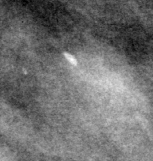
Crop from a digitized film mammogram around one marked abnormality, left breast, CC view, BI-RADS breast density category 3 (scale 1–4).
Calcifications, morphology vascular / coarse; BI-RADS assessment category 2; subtlety rating 3 on a 1 (subtle) to 5 (obvious) scale; benign; no additional work-up was recommended (benign without callback).